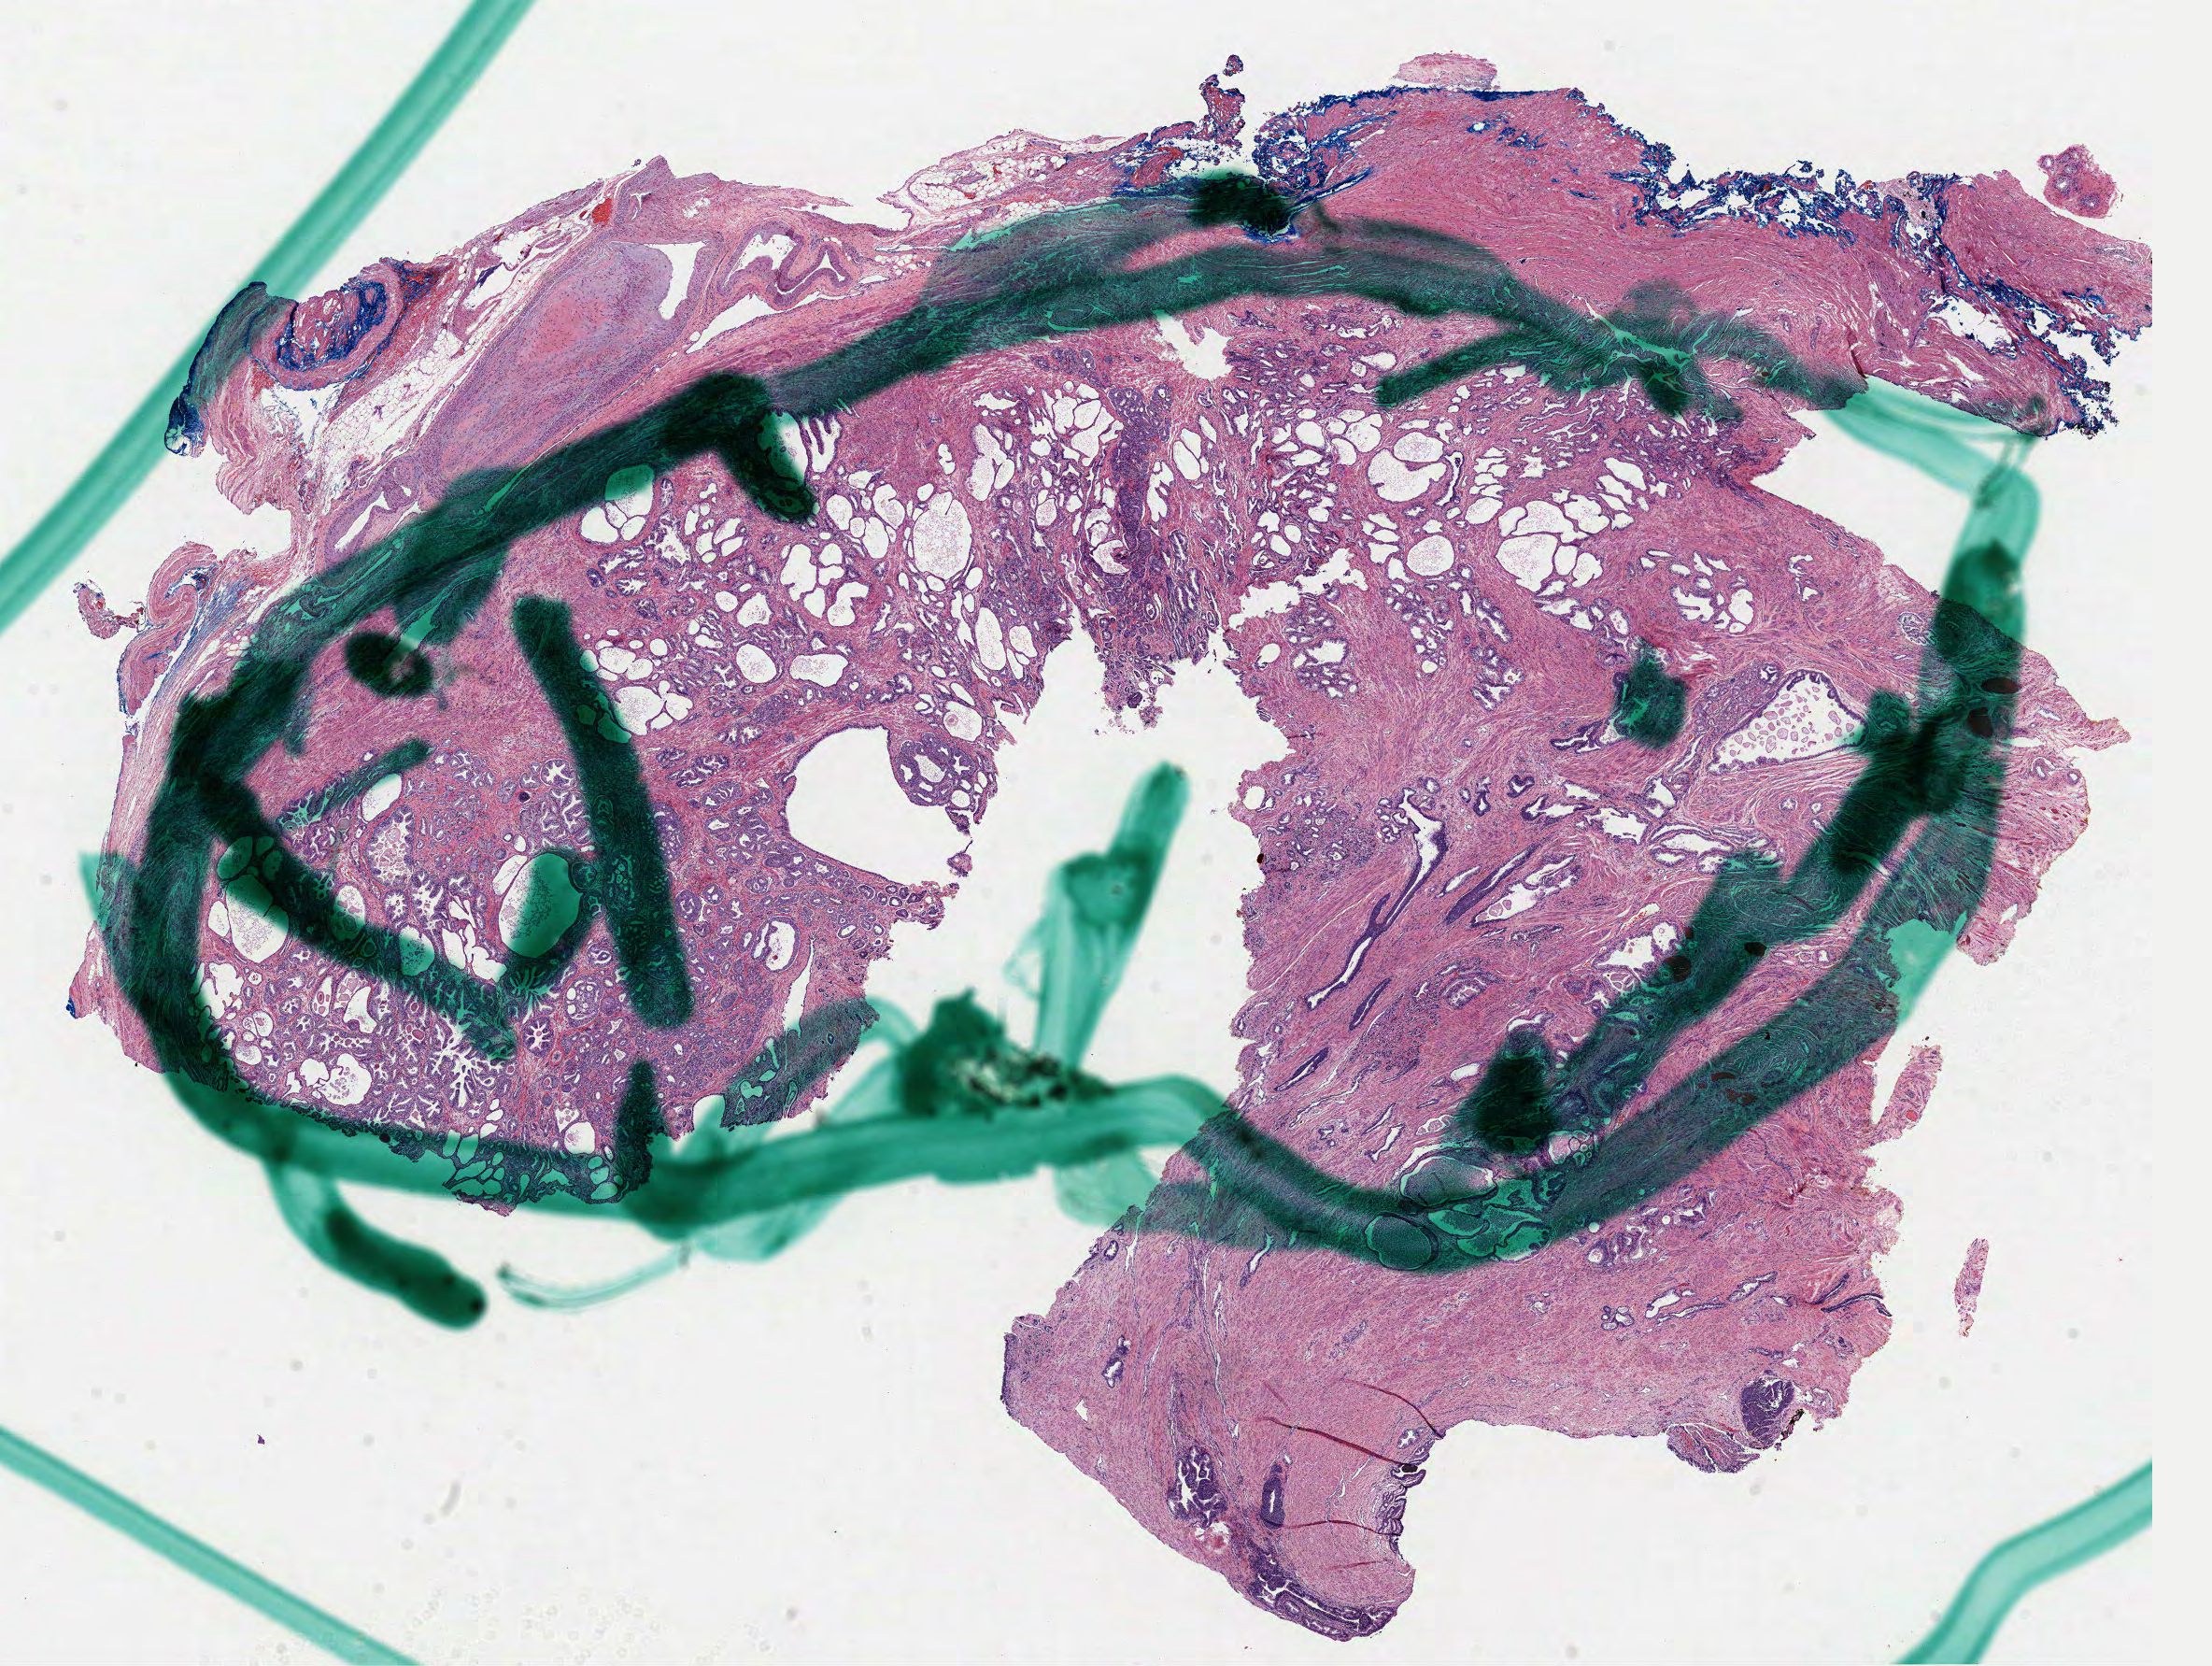
Digitized Hematoxylin and eosin (H&E) stained tissue section (whole slide), low-resolution overview of the scanned area, about 19.1 x 14.4 mm (from a 40x scan). FFPE section. Primary tumour sample from the prostate. Patient: male, age at initial diagnosis 53 years. Gleason score: 7 (3+4).
Diagnosis: Acinar cell carcinoma (prostate gland).